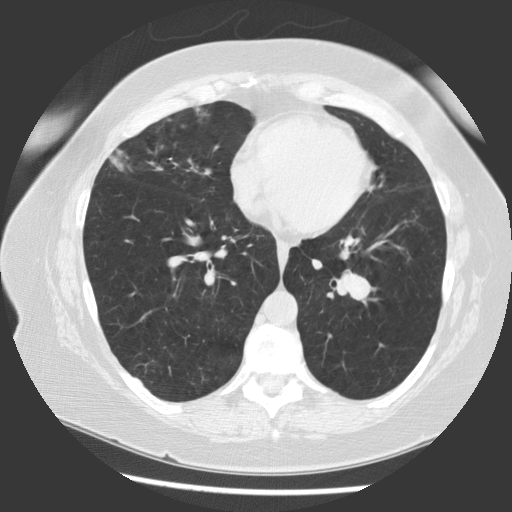
Low-dose screening chest CT, one axial slice; slice 55 of 130 in the series (ordered by position); reconstruction kernel STANDARD; lung window (W 1500 / L -600 HU); 2.5 mm slice thickness; 512 × 512 image matrix.
Annotated regions visible in this slice (manually delineated by an expert):
- lesion 1 (tumor, hilum of left lung): bounding box [x1, y1, x2, y2] px = [342, 274, 372, 301]